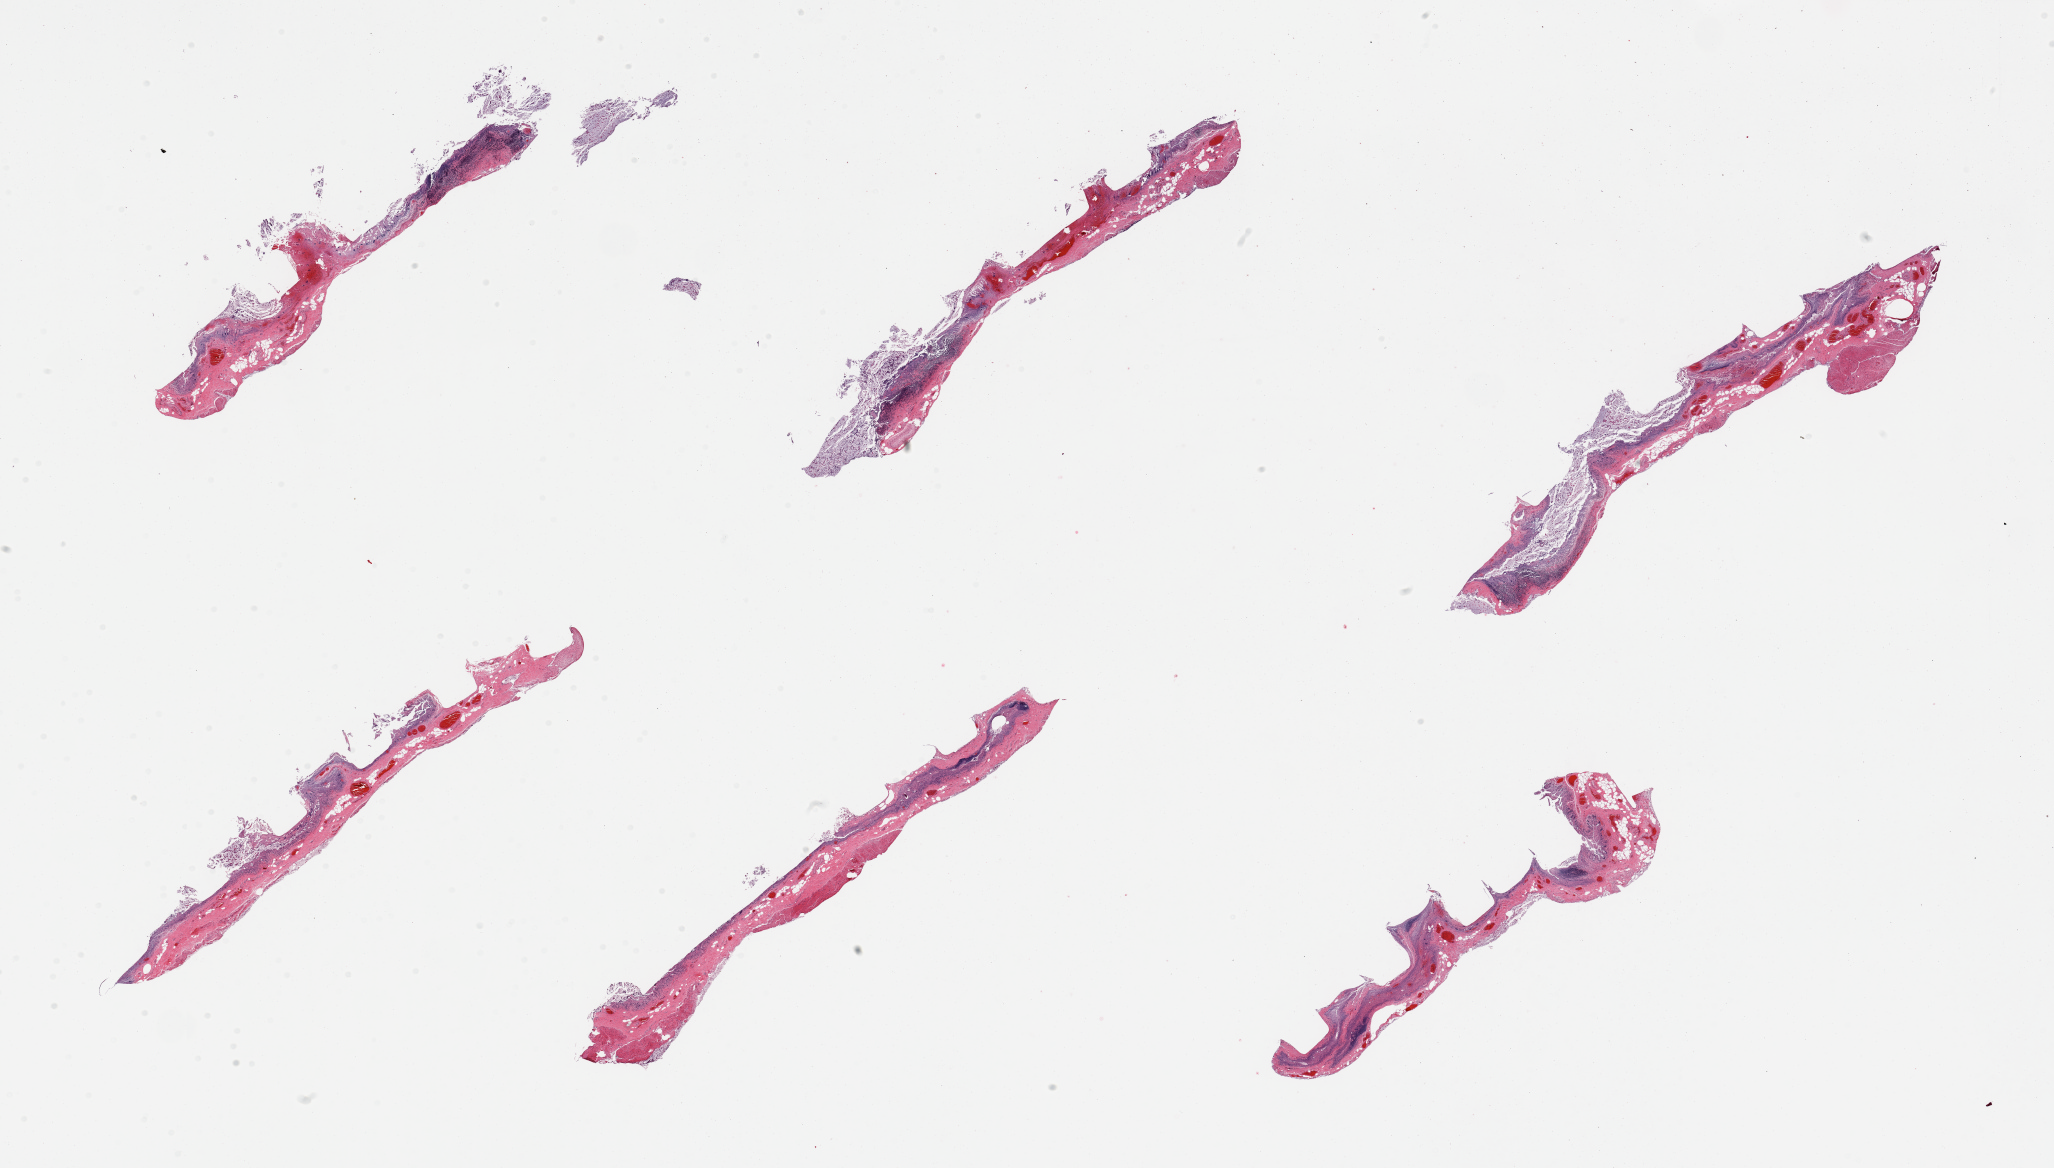
Haematoxylin and eosin whole-slide image, shown as a low-resolution overview of the whole scanned area (about 32.5 x 18.5 mm, slide scanned at 20x), PAXgene-fixed, paraffin-embedded tissue, sampled site (target tissue): ileum, tissue donor sample. Male donor.
• reviewer comment on this tissue sample: 6 pieces, mucosal glandular elements totally autolyzed; ~20% of tissue is residual lymphoid aggregates